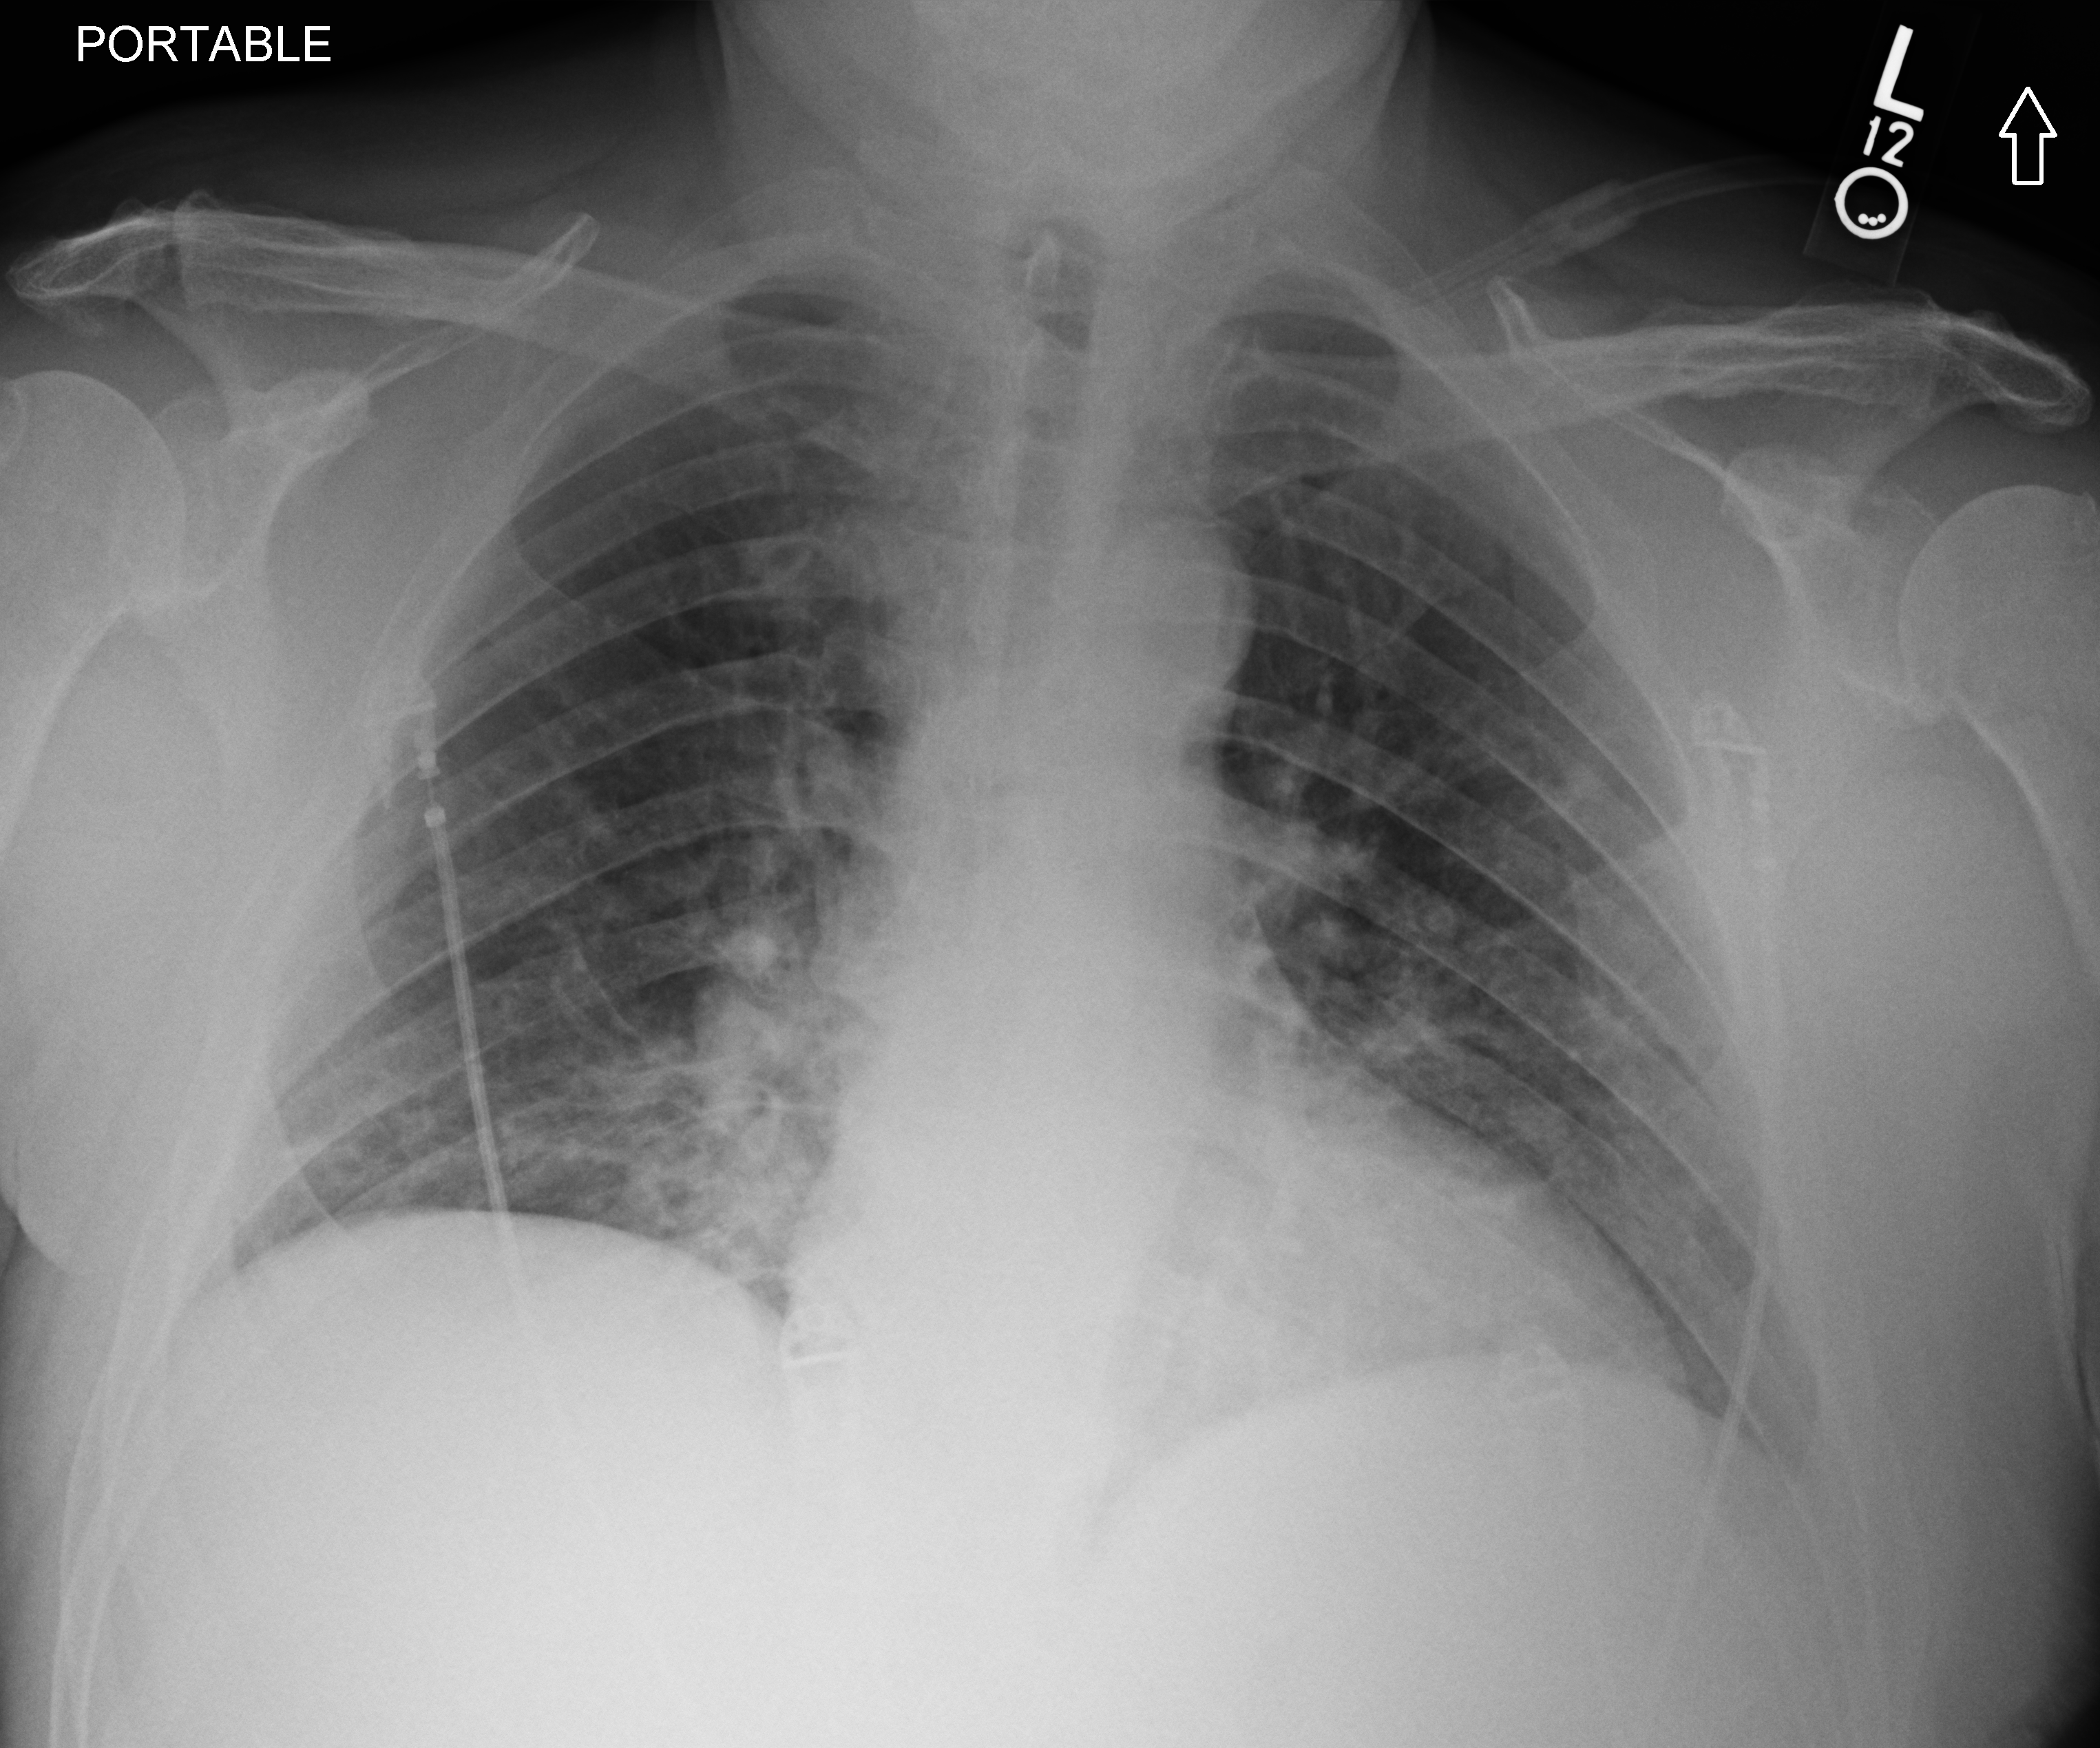
Portable chest radiograph. Patient hospitalised with COVID-19; male, aged 60–74 years.
Hospital-stay facts (about this admission, not read from this image; timing relative to this image not recorded): length of hospital stay: 16 days.